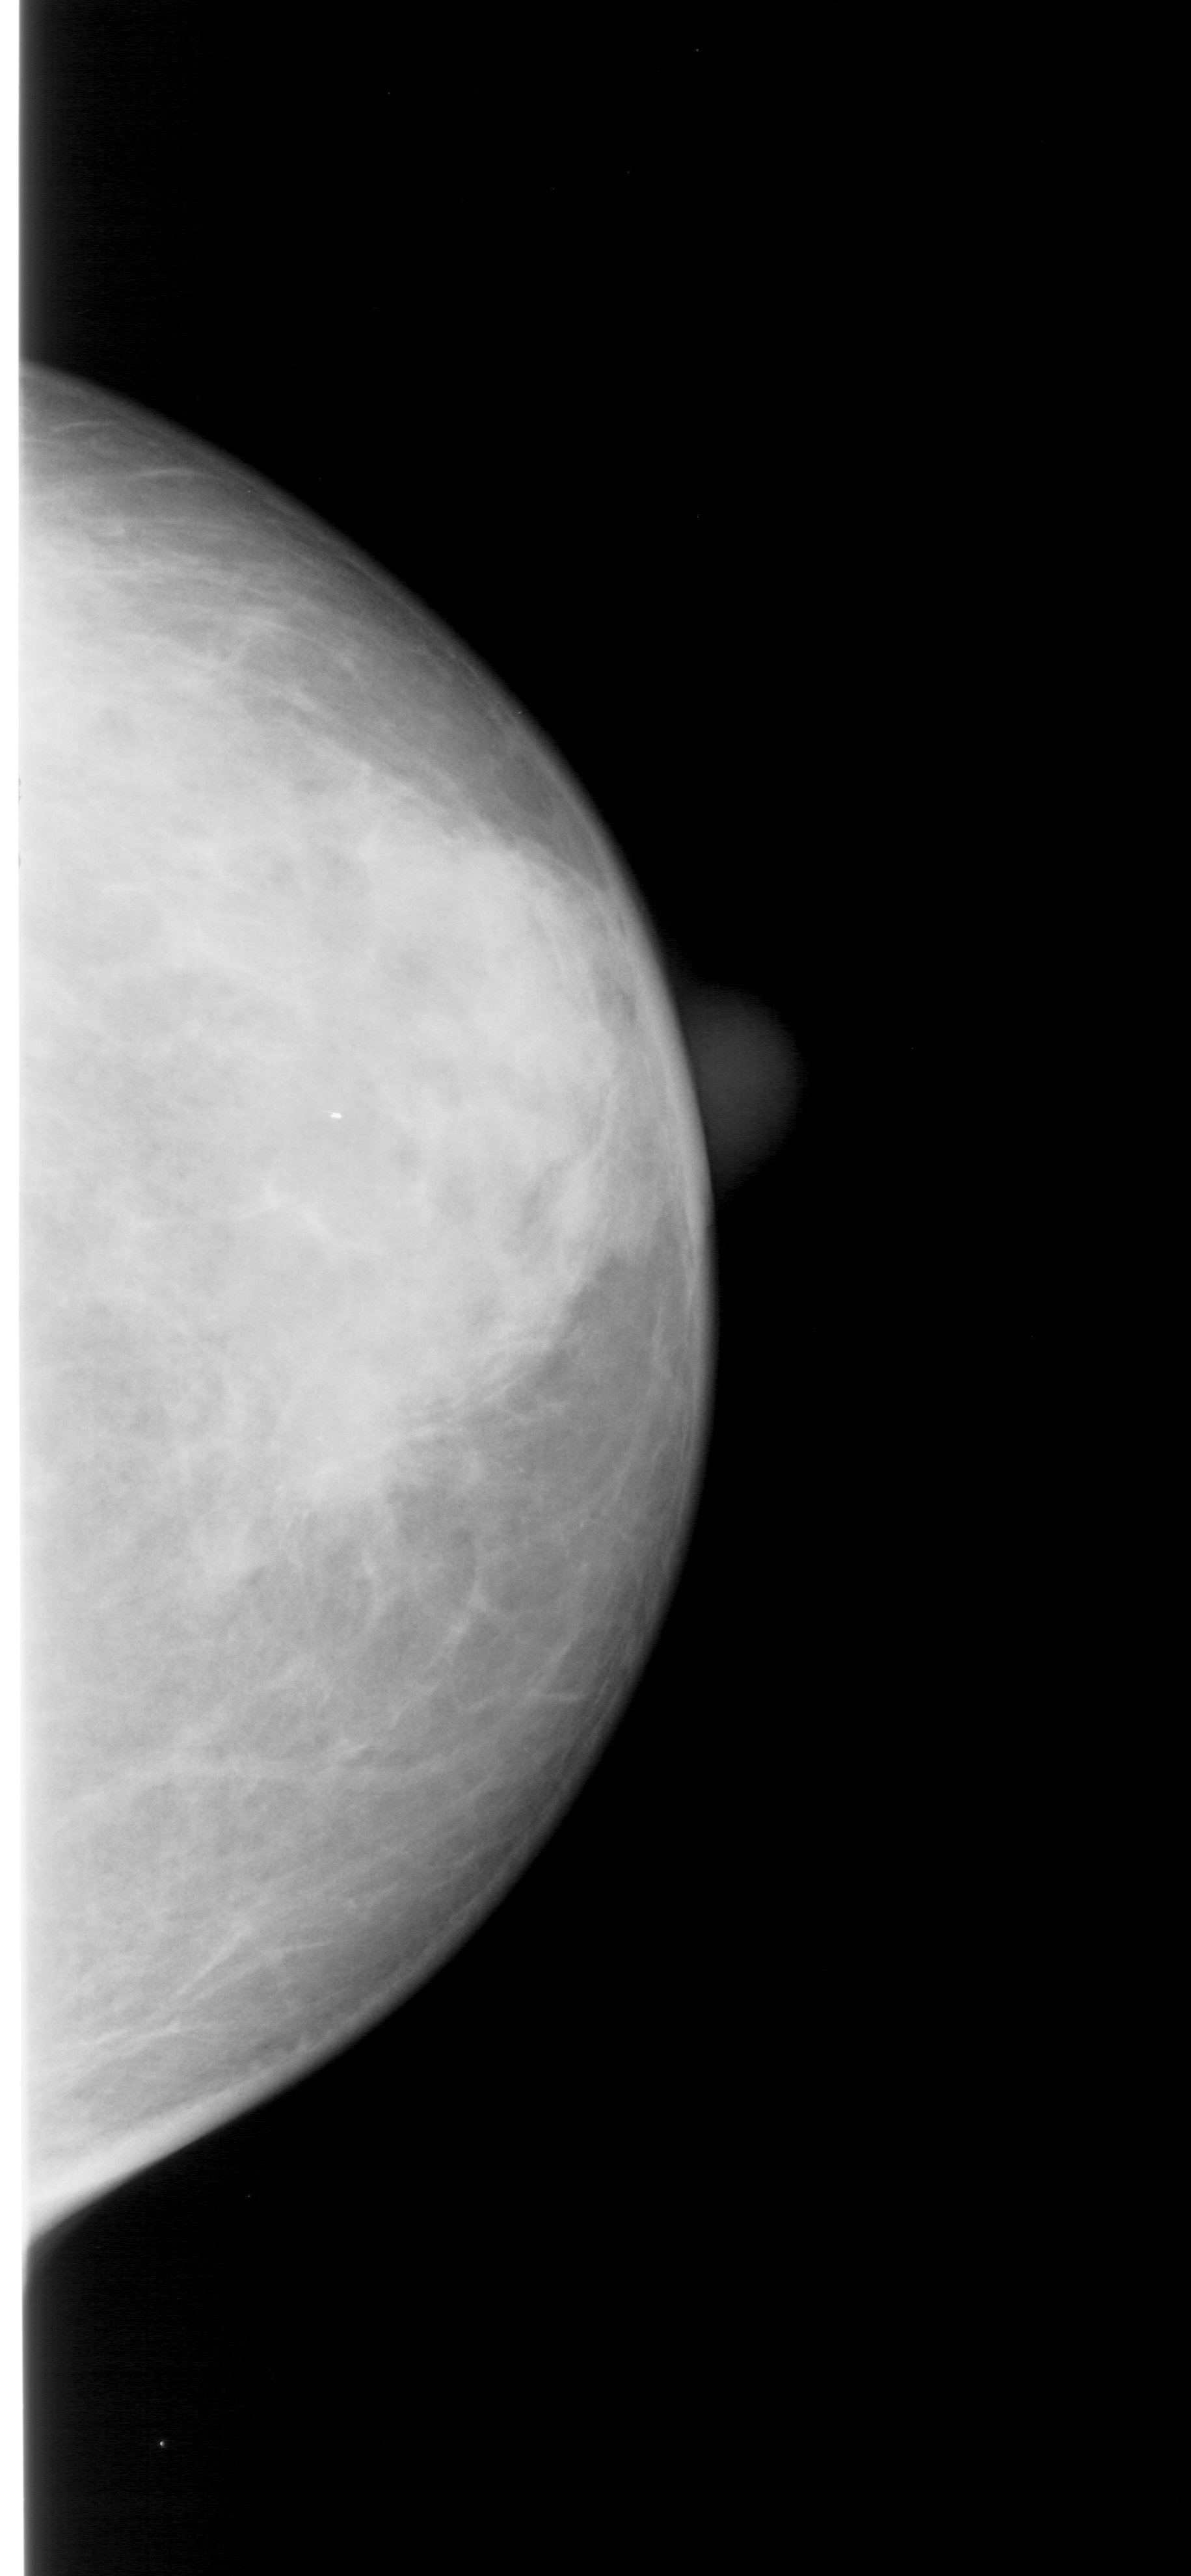
Digitized screen-film mammogram; right breast; craniocaudal (CC) view; breast composition: extremely dense (BI-RADS density category 4 of 4); 1191 × 2576 image matrix.
Expert-marked regions of interest on this image (one box per marked abnormality):
- calcifications, morphology pleomorphic, distribution clustered; BI-RADS assessment category 5; subtlety rating 3 on a 1 (subtle) to 5 (obvious) scale; pathology (as recorded): malignant: bounding box <163,1311,644,1682> (left, top, right, bottom; pixels)